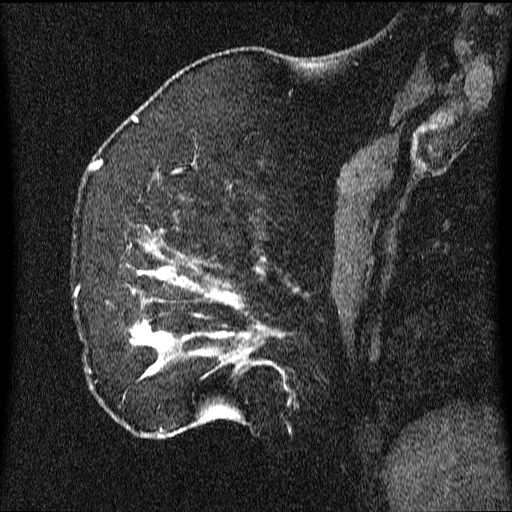
Breast MRI (dynamic contrast-enhanced), one sagittal slice. Position 17 of 64 along the scan axis. Dynamic contrast-enhanced series, image 2 of 3 at this slice position (ordered by acquisition). 1.5 T. TE 4.2 ms, TR 9.1 ms. 2.2 mm slice thickness. 512 × 512 image matrix, field of view 180 × 180 mm. Female patient, age 52 years.
Annotated regions visible in this slice (semi-automatically segmented with operator editing):
- analysis volume of interest (the breast-tissue region the enhancement analysis was run in; not a lesion): bounding box (x1, y1, x2, y2) in pixels: (74, 203, 350, 438)
- tumour enhancement mask (voxels above the 70 % enhancement threshold inside the analysis volume of interest): (76, 228, 286, 437)